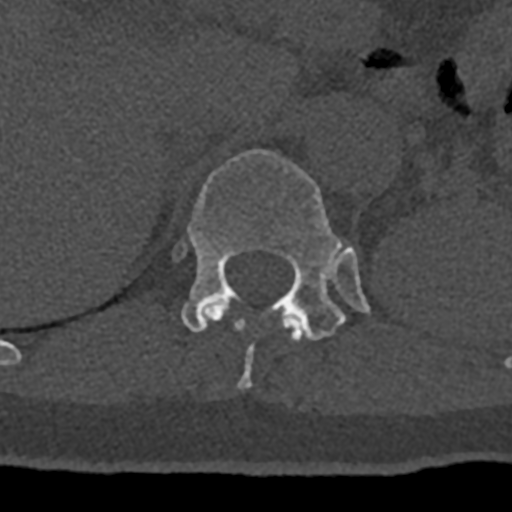
CT including the spine, one axial slice; slice 509 of 797 in the series (ordered by position); reconstruction kernel Br40s/3; bone window (W 1800 / L 400 HU); 0.5 mm slice thickness; 512 × 512 image matrix, field of view 160 × 160 mm. Male patient, age 74 years. From the clinical record (not read from this slice): primary cancer: renal.
Outlined on this slice (semi-automatic segmentation, software-assisted and operator-edited):
- T11 vertebra: bounding box (x1, y1, x2, y2) in pixels: (204, 302, 304, 389)
- T12 vertebra: (174, 149, 370, 341)